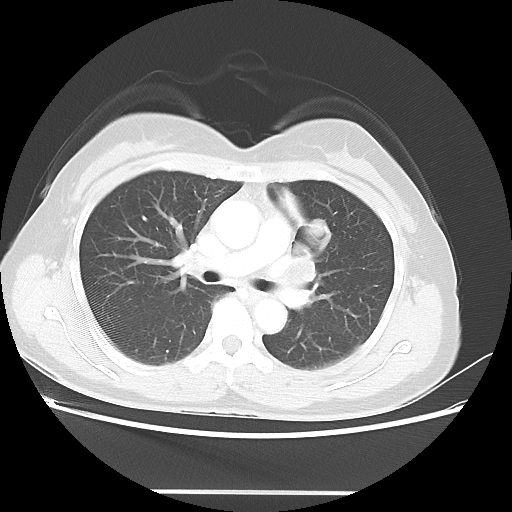
Chest CT, one axial slice. Position 27 of 46 along the scan axis. Reconstruction kernel LUNG. 100 kVp. Lung window (W 1500 / L -600 HU). 5 mm slice thickness. 512 × 512 image matrix. Patient: female, 50 years. Case-level facts recorded for this patient, not image findings: clinical TNM (as recorded): T1c N1 M0; histopathological grade: G3.
Annotated regions visible in this slice (rectangle marked by the reading radiologist):
- lung tumour (recorded histology: adenocarcinoma): bounding box <306,214,332,250> (left, top, right, bottom; pixels)